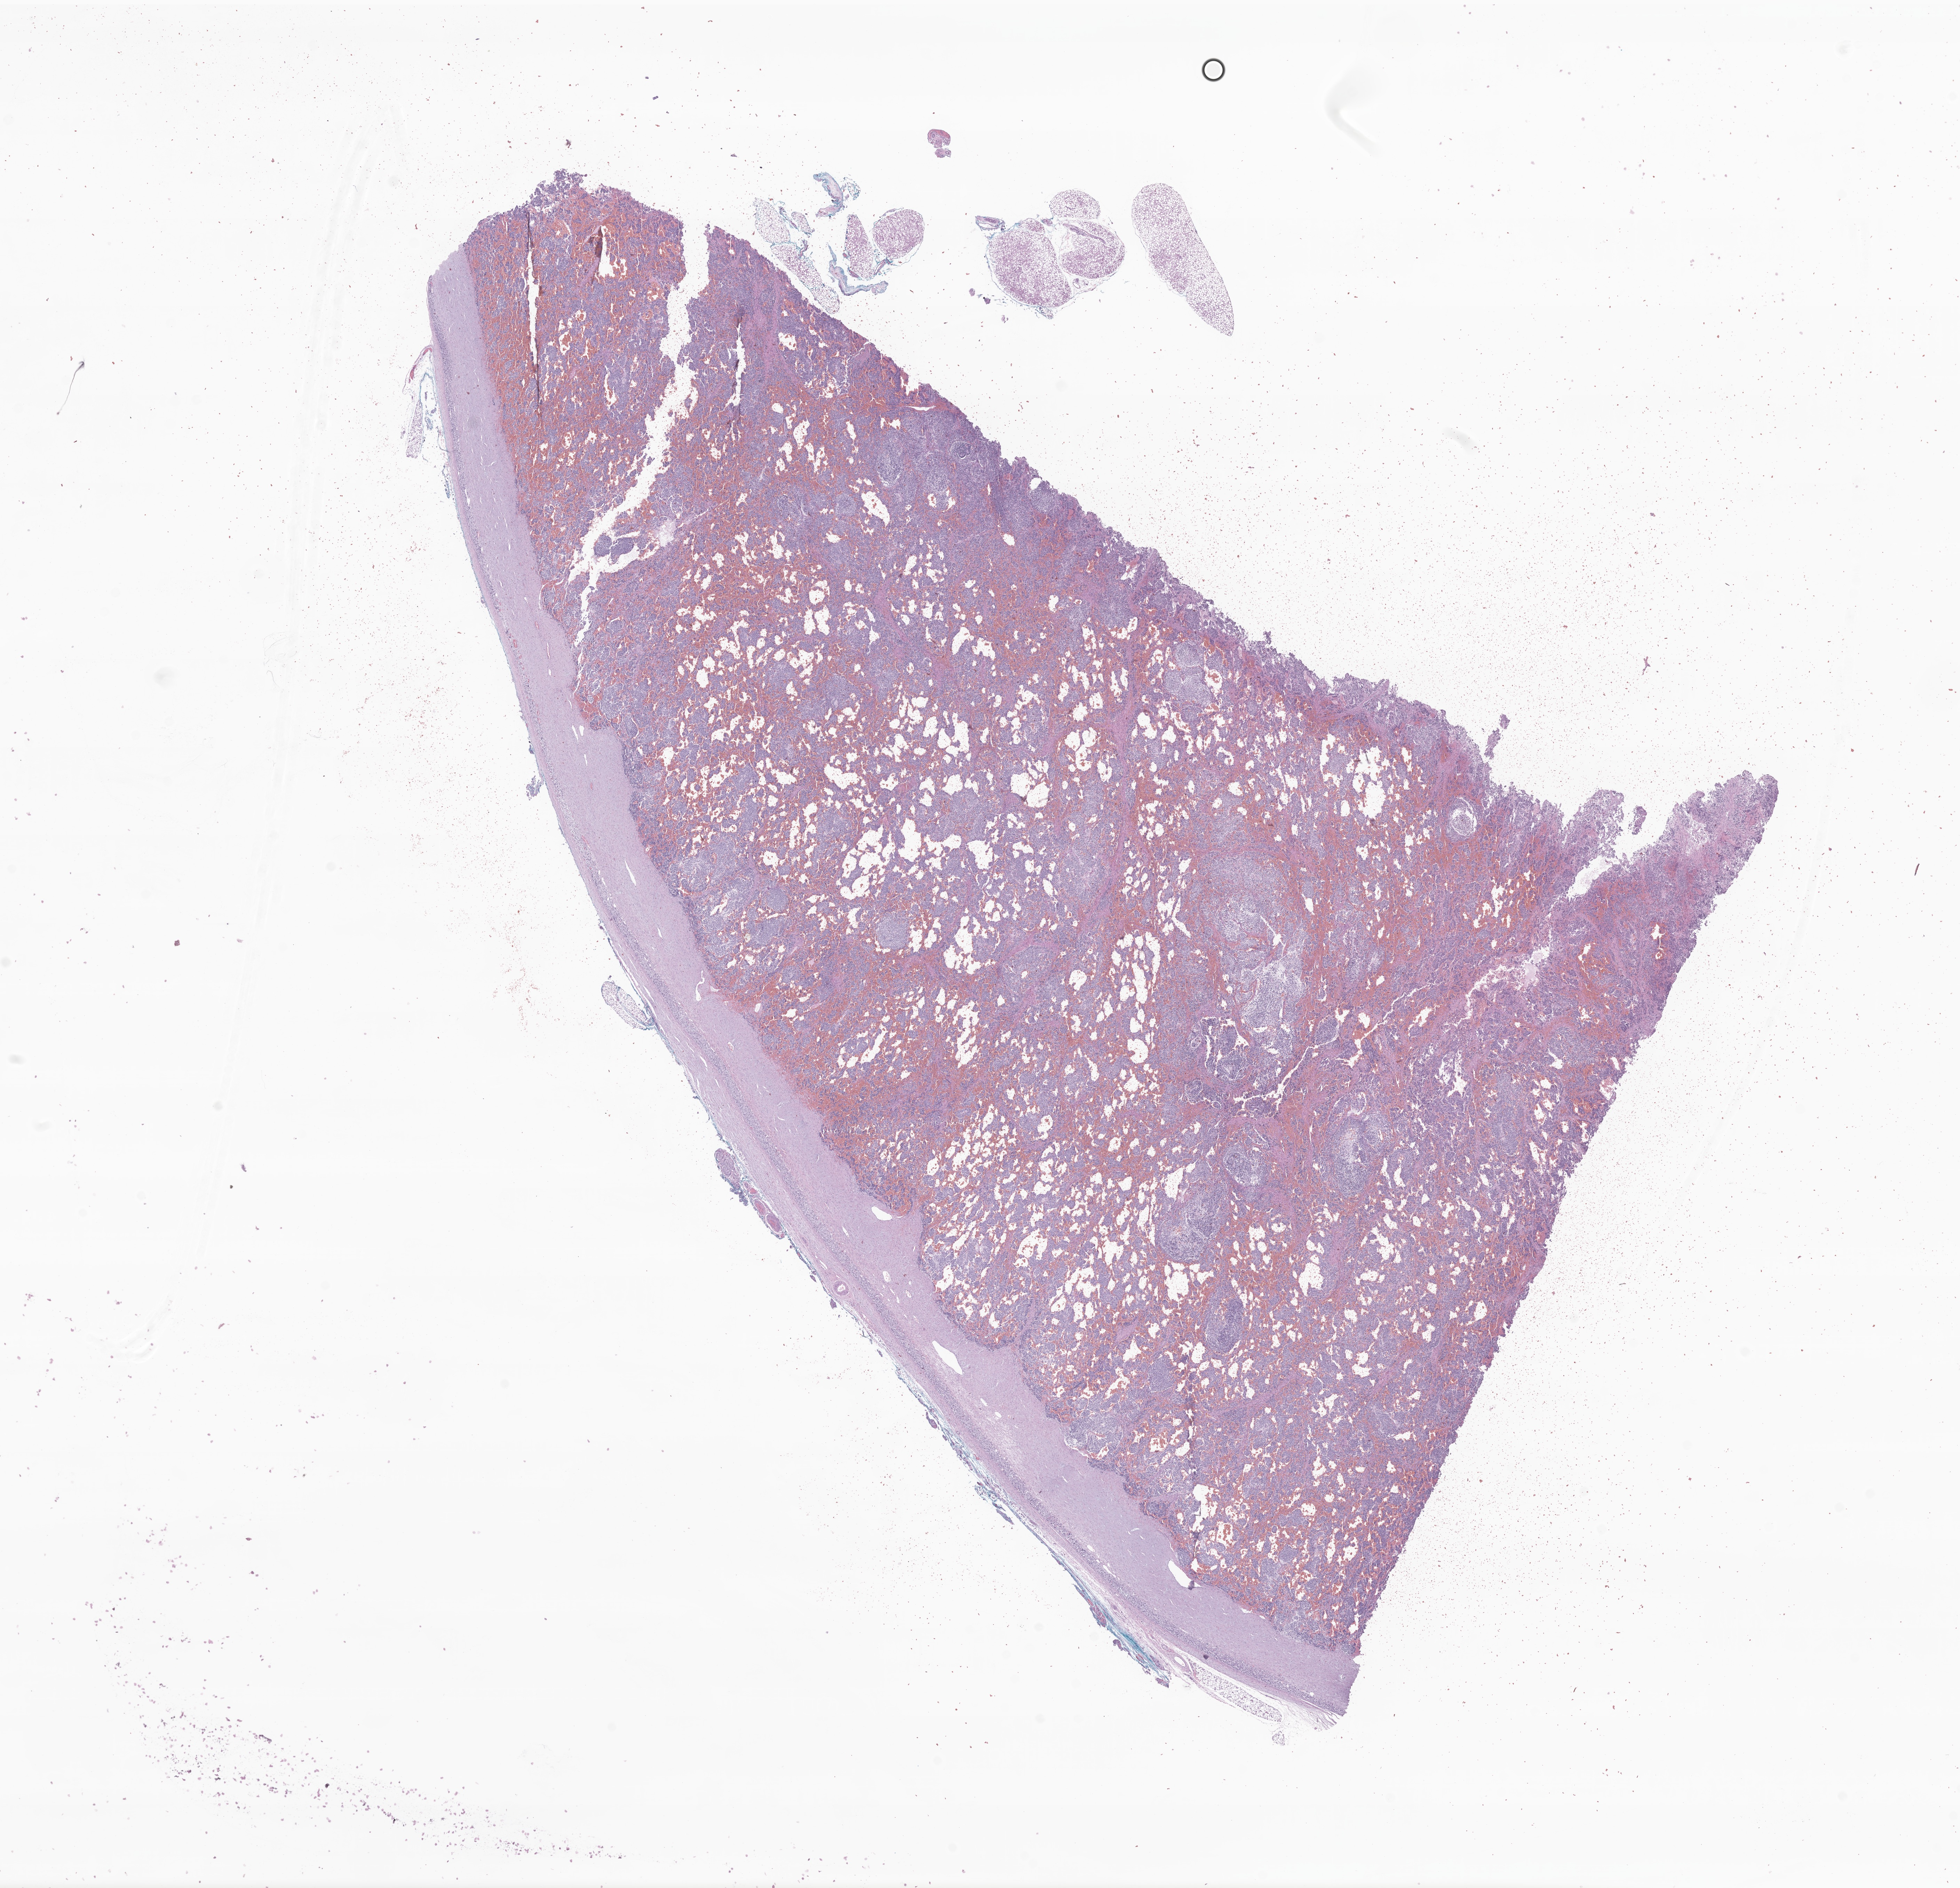
Haematoxylin and eosin whole-slide image of tumor tissue from the adrenal gland — whole scanned area (about 23.7 x 22.9 mm) shown as a low-resolution overview; FFPE section. Patient female; age 49 days.
* diagnosis: Neuroblastoma, NOS